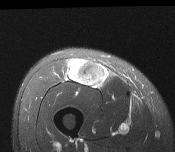
MRI of an extremity soft-tissue mass, one axial slice; T2-weighted fat-saturated; MR volume resampled by the dataset authors to the PET/CT grid (not the native acquisition matrix); 175 × 152 image matrix. Male patient. From the clinical record (not read from this slice): histological type: pleiomorphic leiomyosarcoma; grade: intermediate; site of the primary tumour: right thigh.
Outlined on this slice (expert contour drawn on MRI and transferred to this co-registered scan by the dataset authors):
- gross tumour volume including surrounding oedema: bounding box (x1, y1, x2, y2) in pixels: (69, 58, 107, 87)